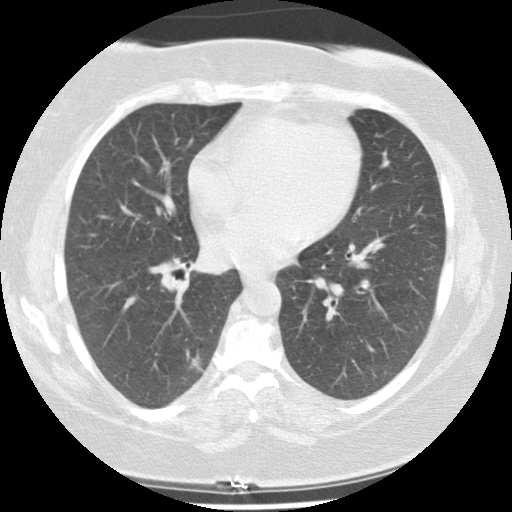
Chest CT (low-dose screening protocol), one axial image; second screening round (one year after baseline); lung window (W 1500 / L -600 HU); 2.5 mm slice thickness. Female participant, aged 58 years at enrolment. Current smoker at enrolment.
Expert-annotated lung lesion, bounding box (x1, y1, x2, y2) in pixels: (161, 331, 222, 398). The screening reader recorded 4 non-calcified nodules or masses ≥4 mm on this exam (right lower lobe, right middle lobe, right upper lobe, right middle lobe); which of them this box marks is not recorded. Later outcome: lung cancer diagnosed 299 days after this screen — adenocarcinoma, NOS, right lower lobe, stage IIIA (AJCC 6th edition), 25 mm at pathology.